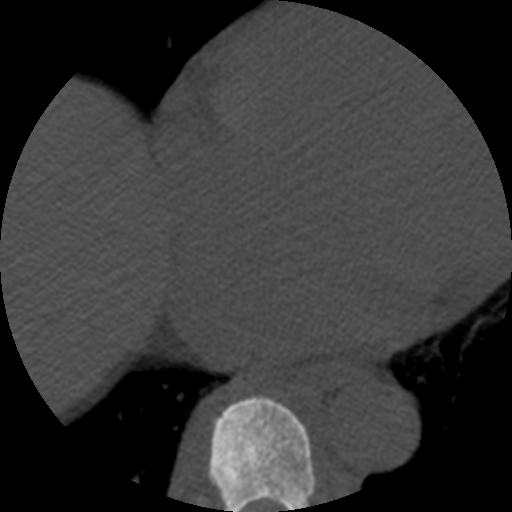
CT including the spine, one axial slice. Position 313 of 508 along the scan axis. Reconstruction kernel STANDARD. 120 kVp. Bone window (W 1800 / L 400 HU). 1.25 mm slice thickness. 512 × 512 image matrix, field of view 160 × 160 mm. Patient age 57 years. Case-level facts recorded for this patient, not image findings: primary cancer: prostate.
Structures marked on this image (semi-automatically segmented with operator editing):
- T8 vertebra: bounding box <208,396,316,512> (left, top, right, bottom; pixels)